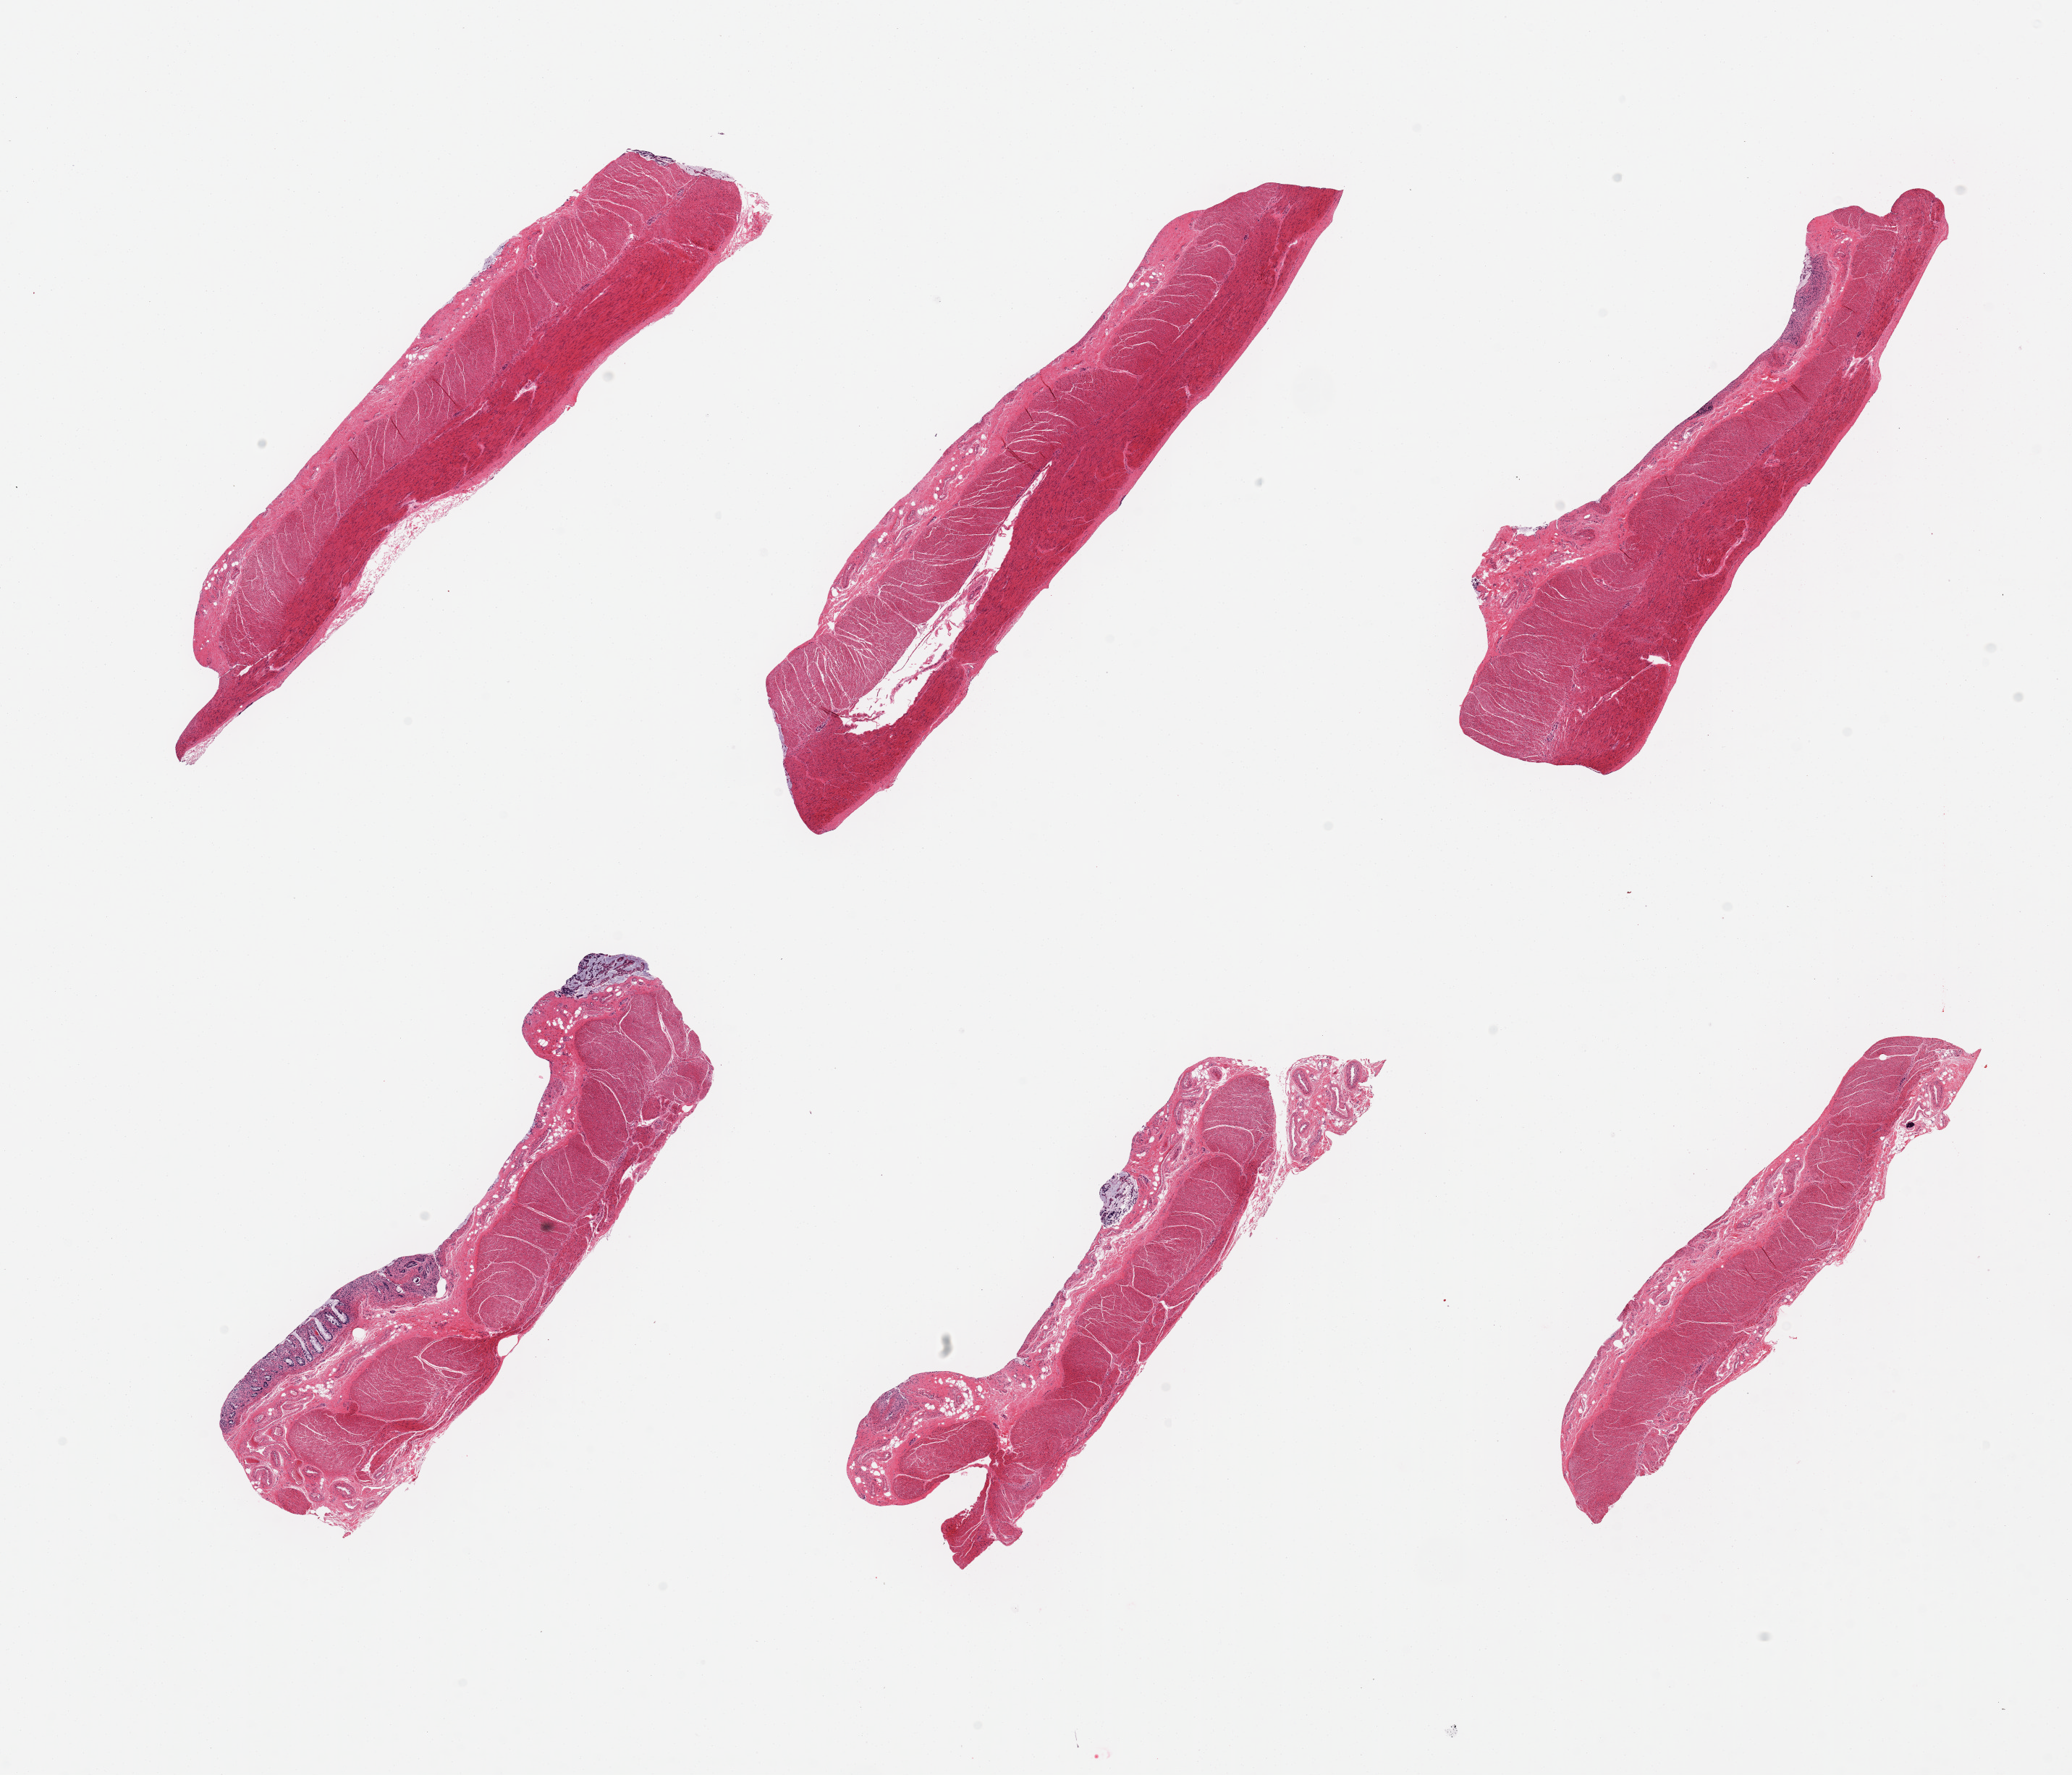
Digitized H&E-stained section — a low-resolution overview of the entire scanned area, about 22.6 x 19.4 mm. PAXgene-fixed paraffin-embedded (PFPE) section. Section of sigmoid colon (target tissue). Donor tissue sample.
• pathologist's review note for this sample: 6 pieces; predominantly muscularis with some residual mucosa (not target, some)